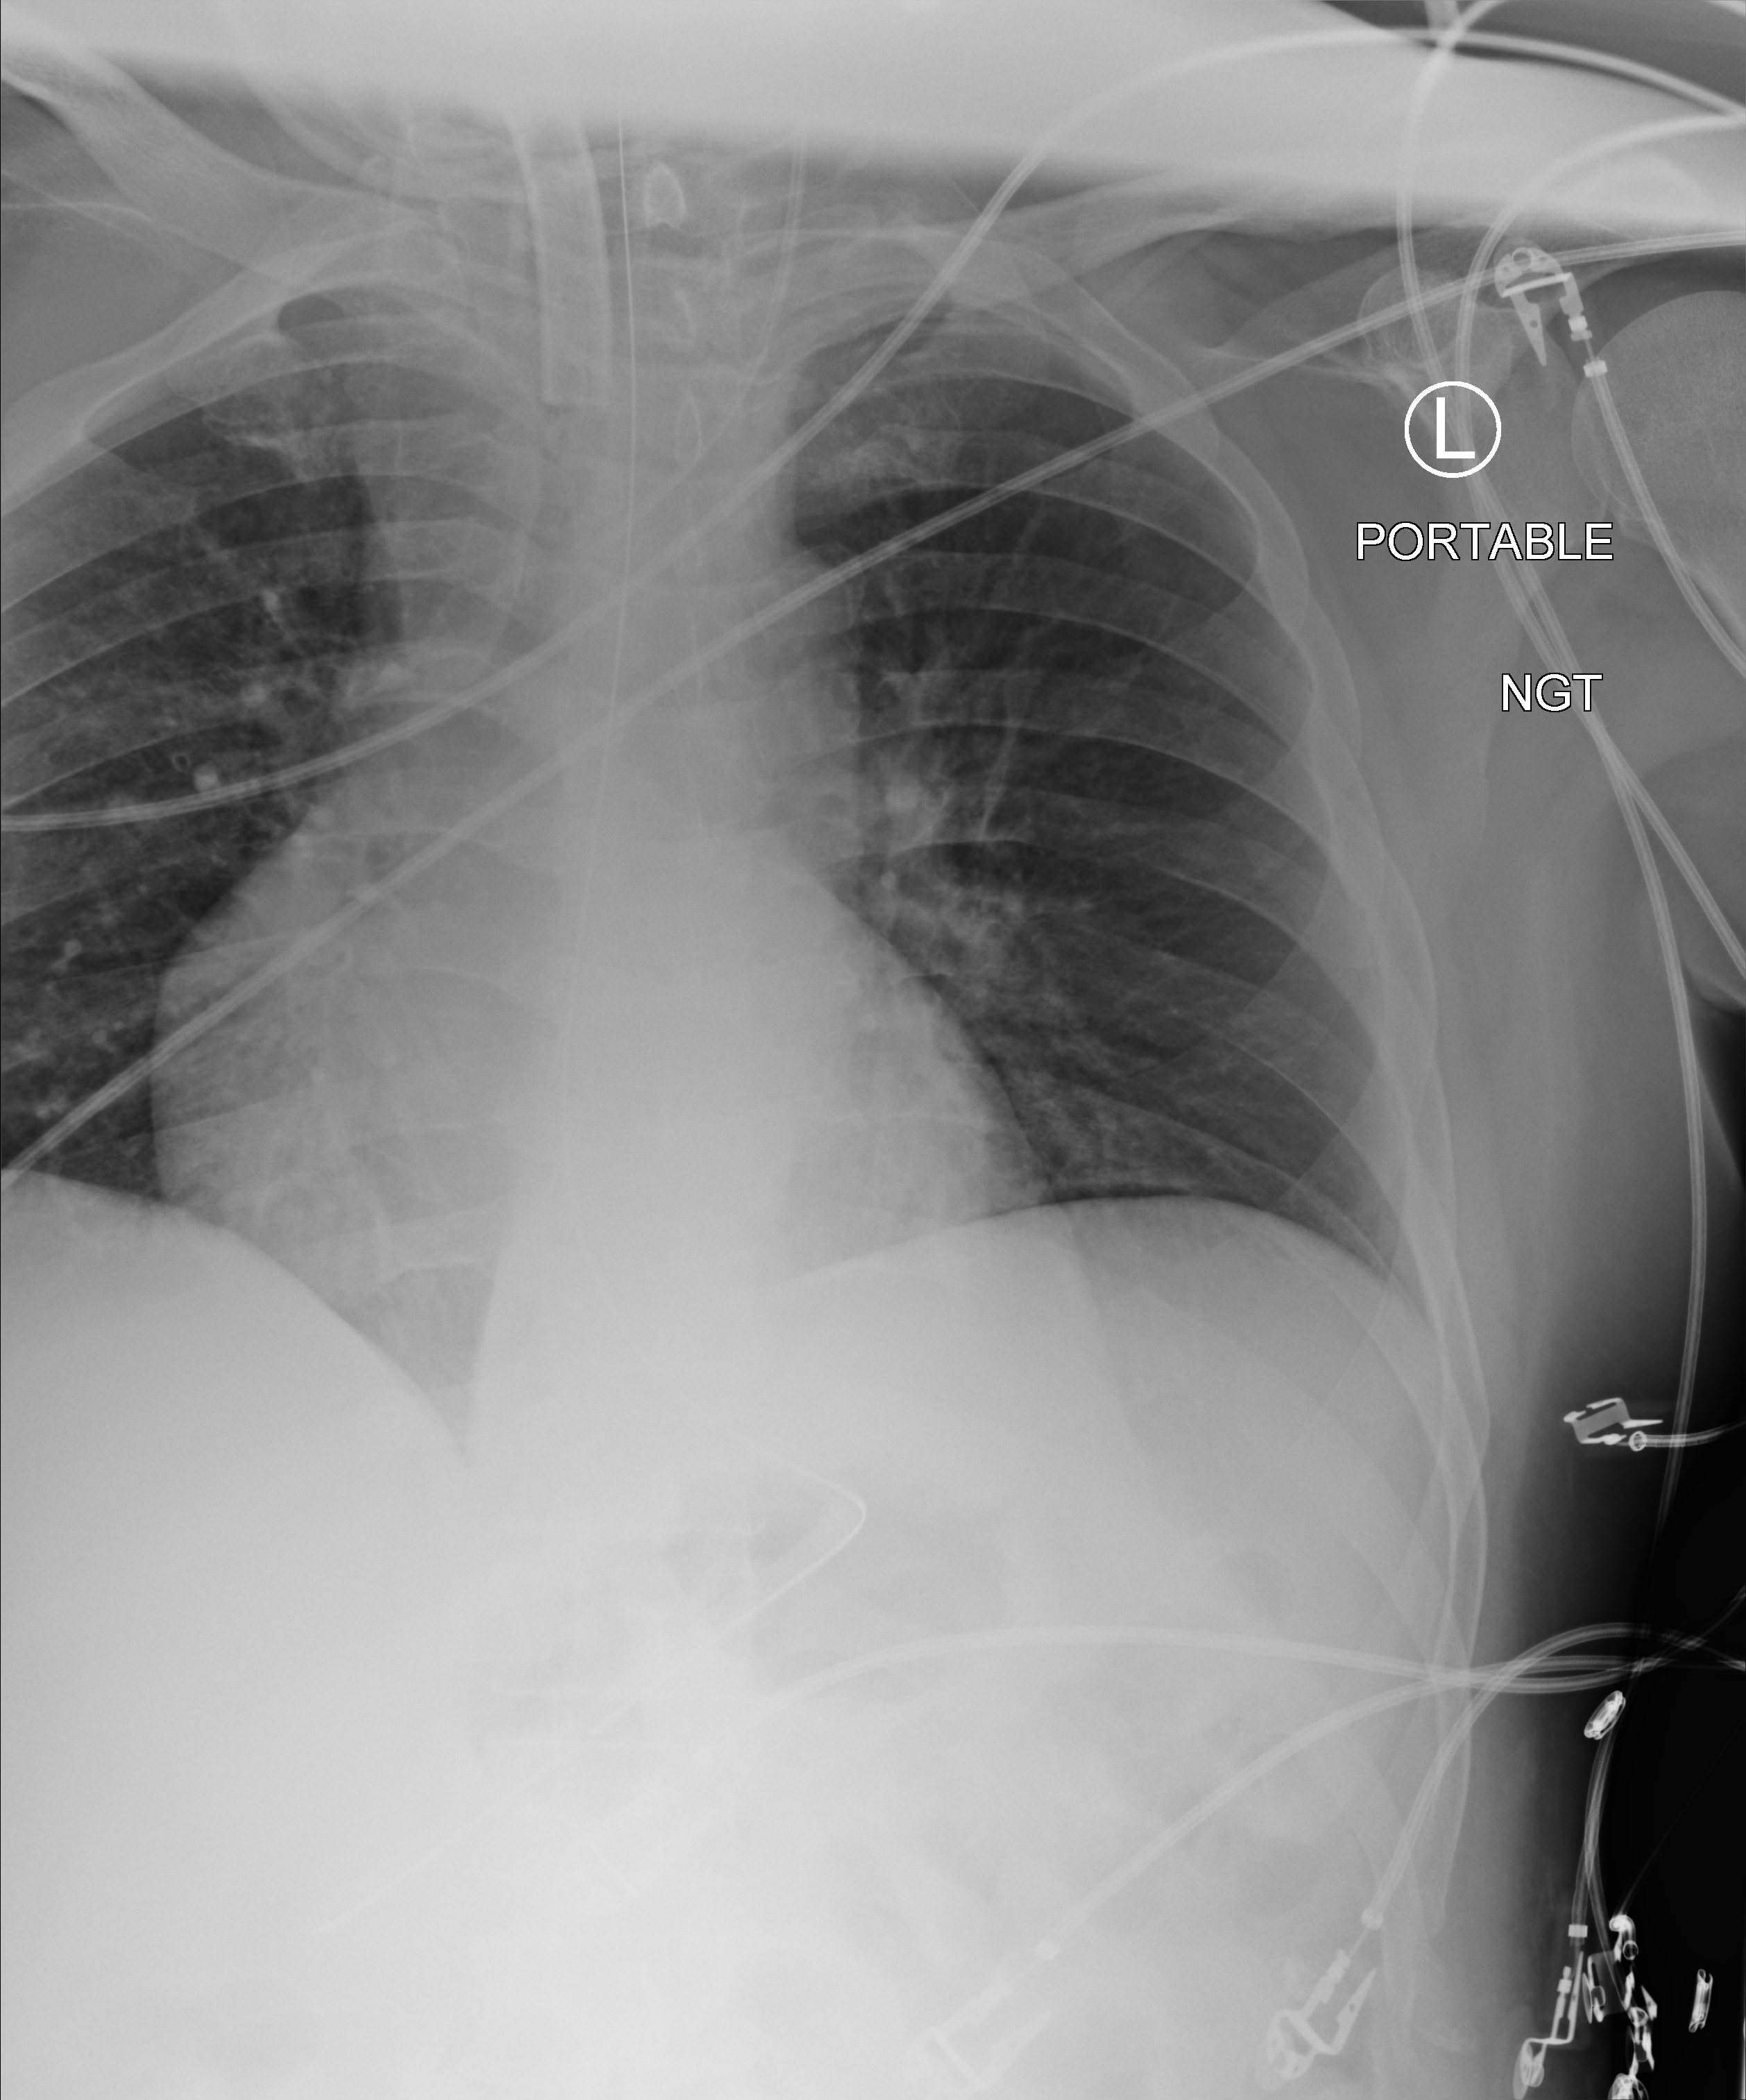
Portable chest radiograph, anteroposterior (AP) projection. Male patient hospitalised with COVID-19, age 18–59 years.
Admission-level facts for this patient (not findings on this image; timing relative to this image not recorded): admitted to intensive care during this hospital stay: yes; mechanically ventilated during this hospital stay: yes.